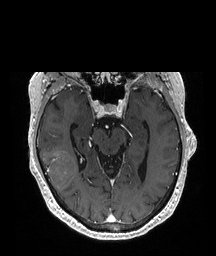
Brain MRI from a brain-tumour surgery series, one axial slice. Slice 128 of 208 in the series (ordered by position). T1-weighted post-contrast. 1 mm slice thickness. 216 × 256 image matrix, field of view 216 × 256 mm. Case-level facts recorded for this patient, not image findings: histopathology: Glioblastoma; WHO grade: 4; IDH mutation: no; tumour location: Right Temporal.
Structures marked on this image (outlined manually by an expert reader):
- tumour: bounding box <43,151,76,193> (left, top, right, bottom; pixels)